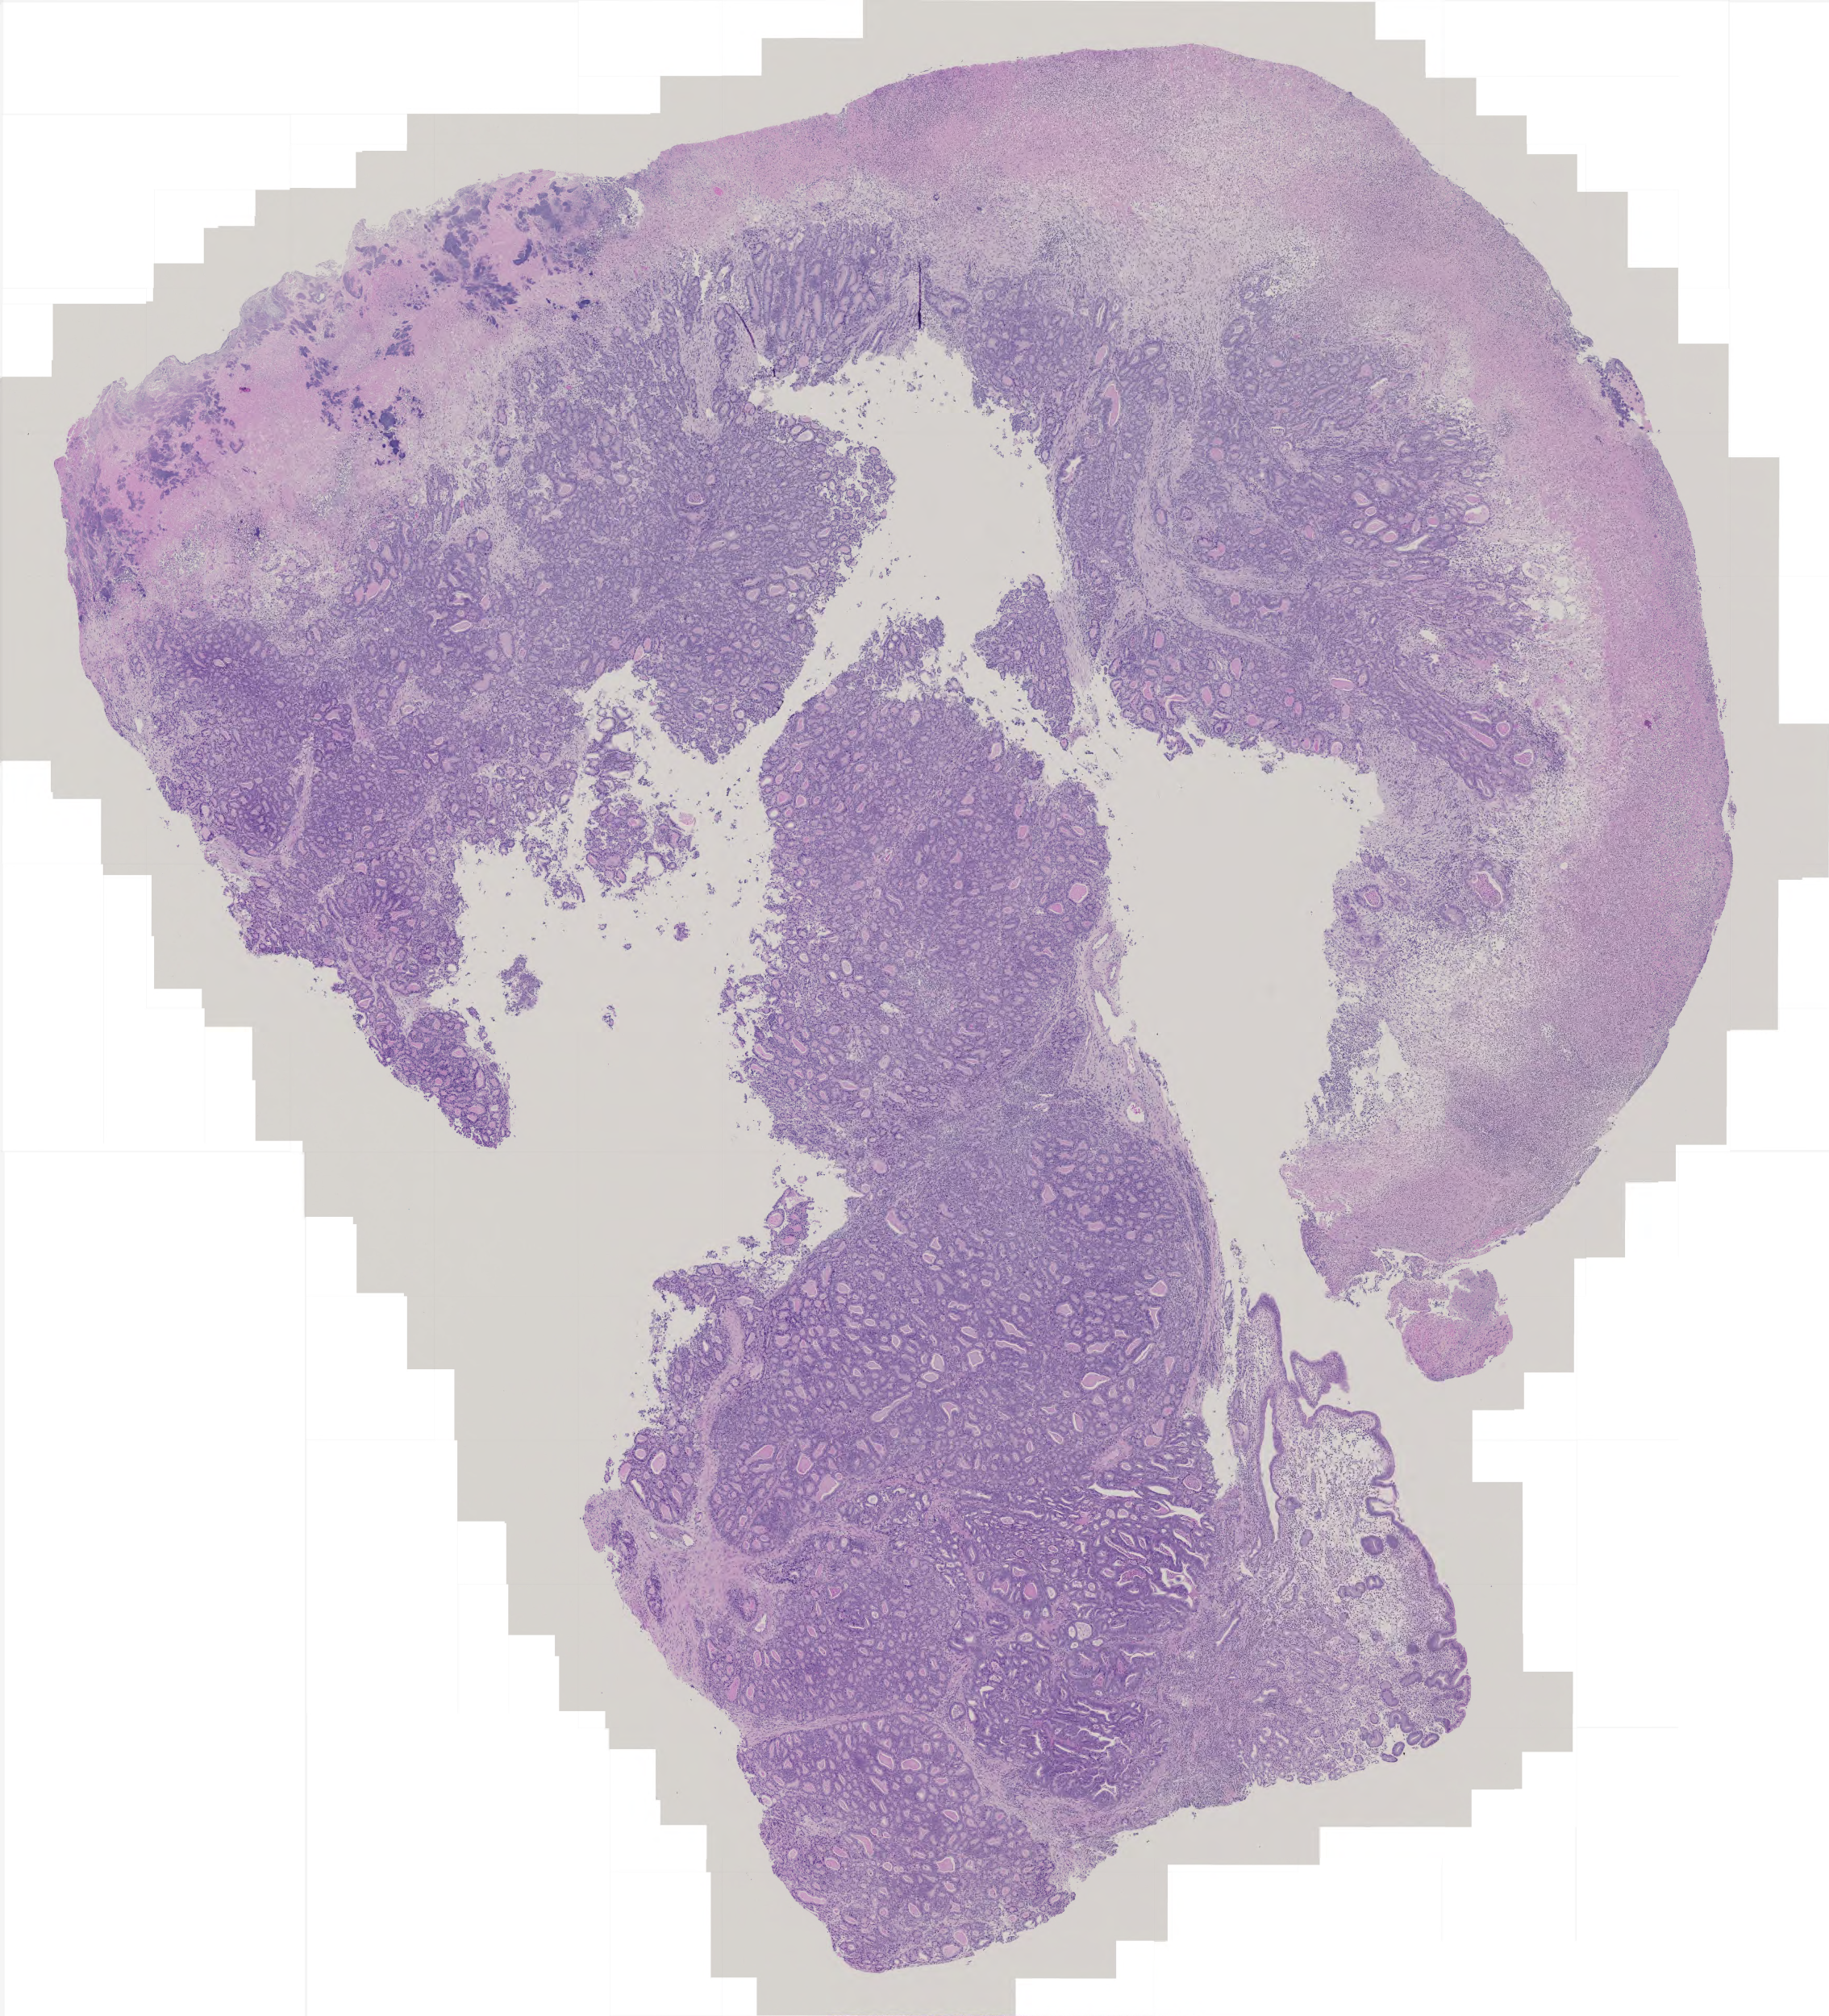
Whole-slide histology image, Hematoxylin and eosin (H&E) stained — low-resolution overview of the scanned area, about 4.5 x 5.0 mm. Formalin-fixed paraffin-embedded (FFPE) diagnostic section. Stomach, primary tumour sample. Female patient; age at initial diagnosis 78 years. Histologic grade: G2 (moderately differentiated).
* lymph nodes positive (case pathology): 3 of 39 examined
* histologic diagnosis: Adenocarcinoma, intestinal type (body of stomach)
* AJCC pathologic stage: II (6th edition)